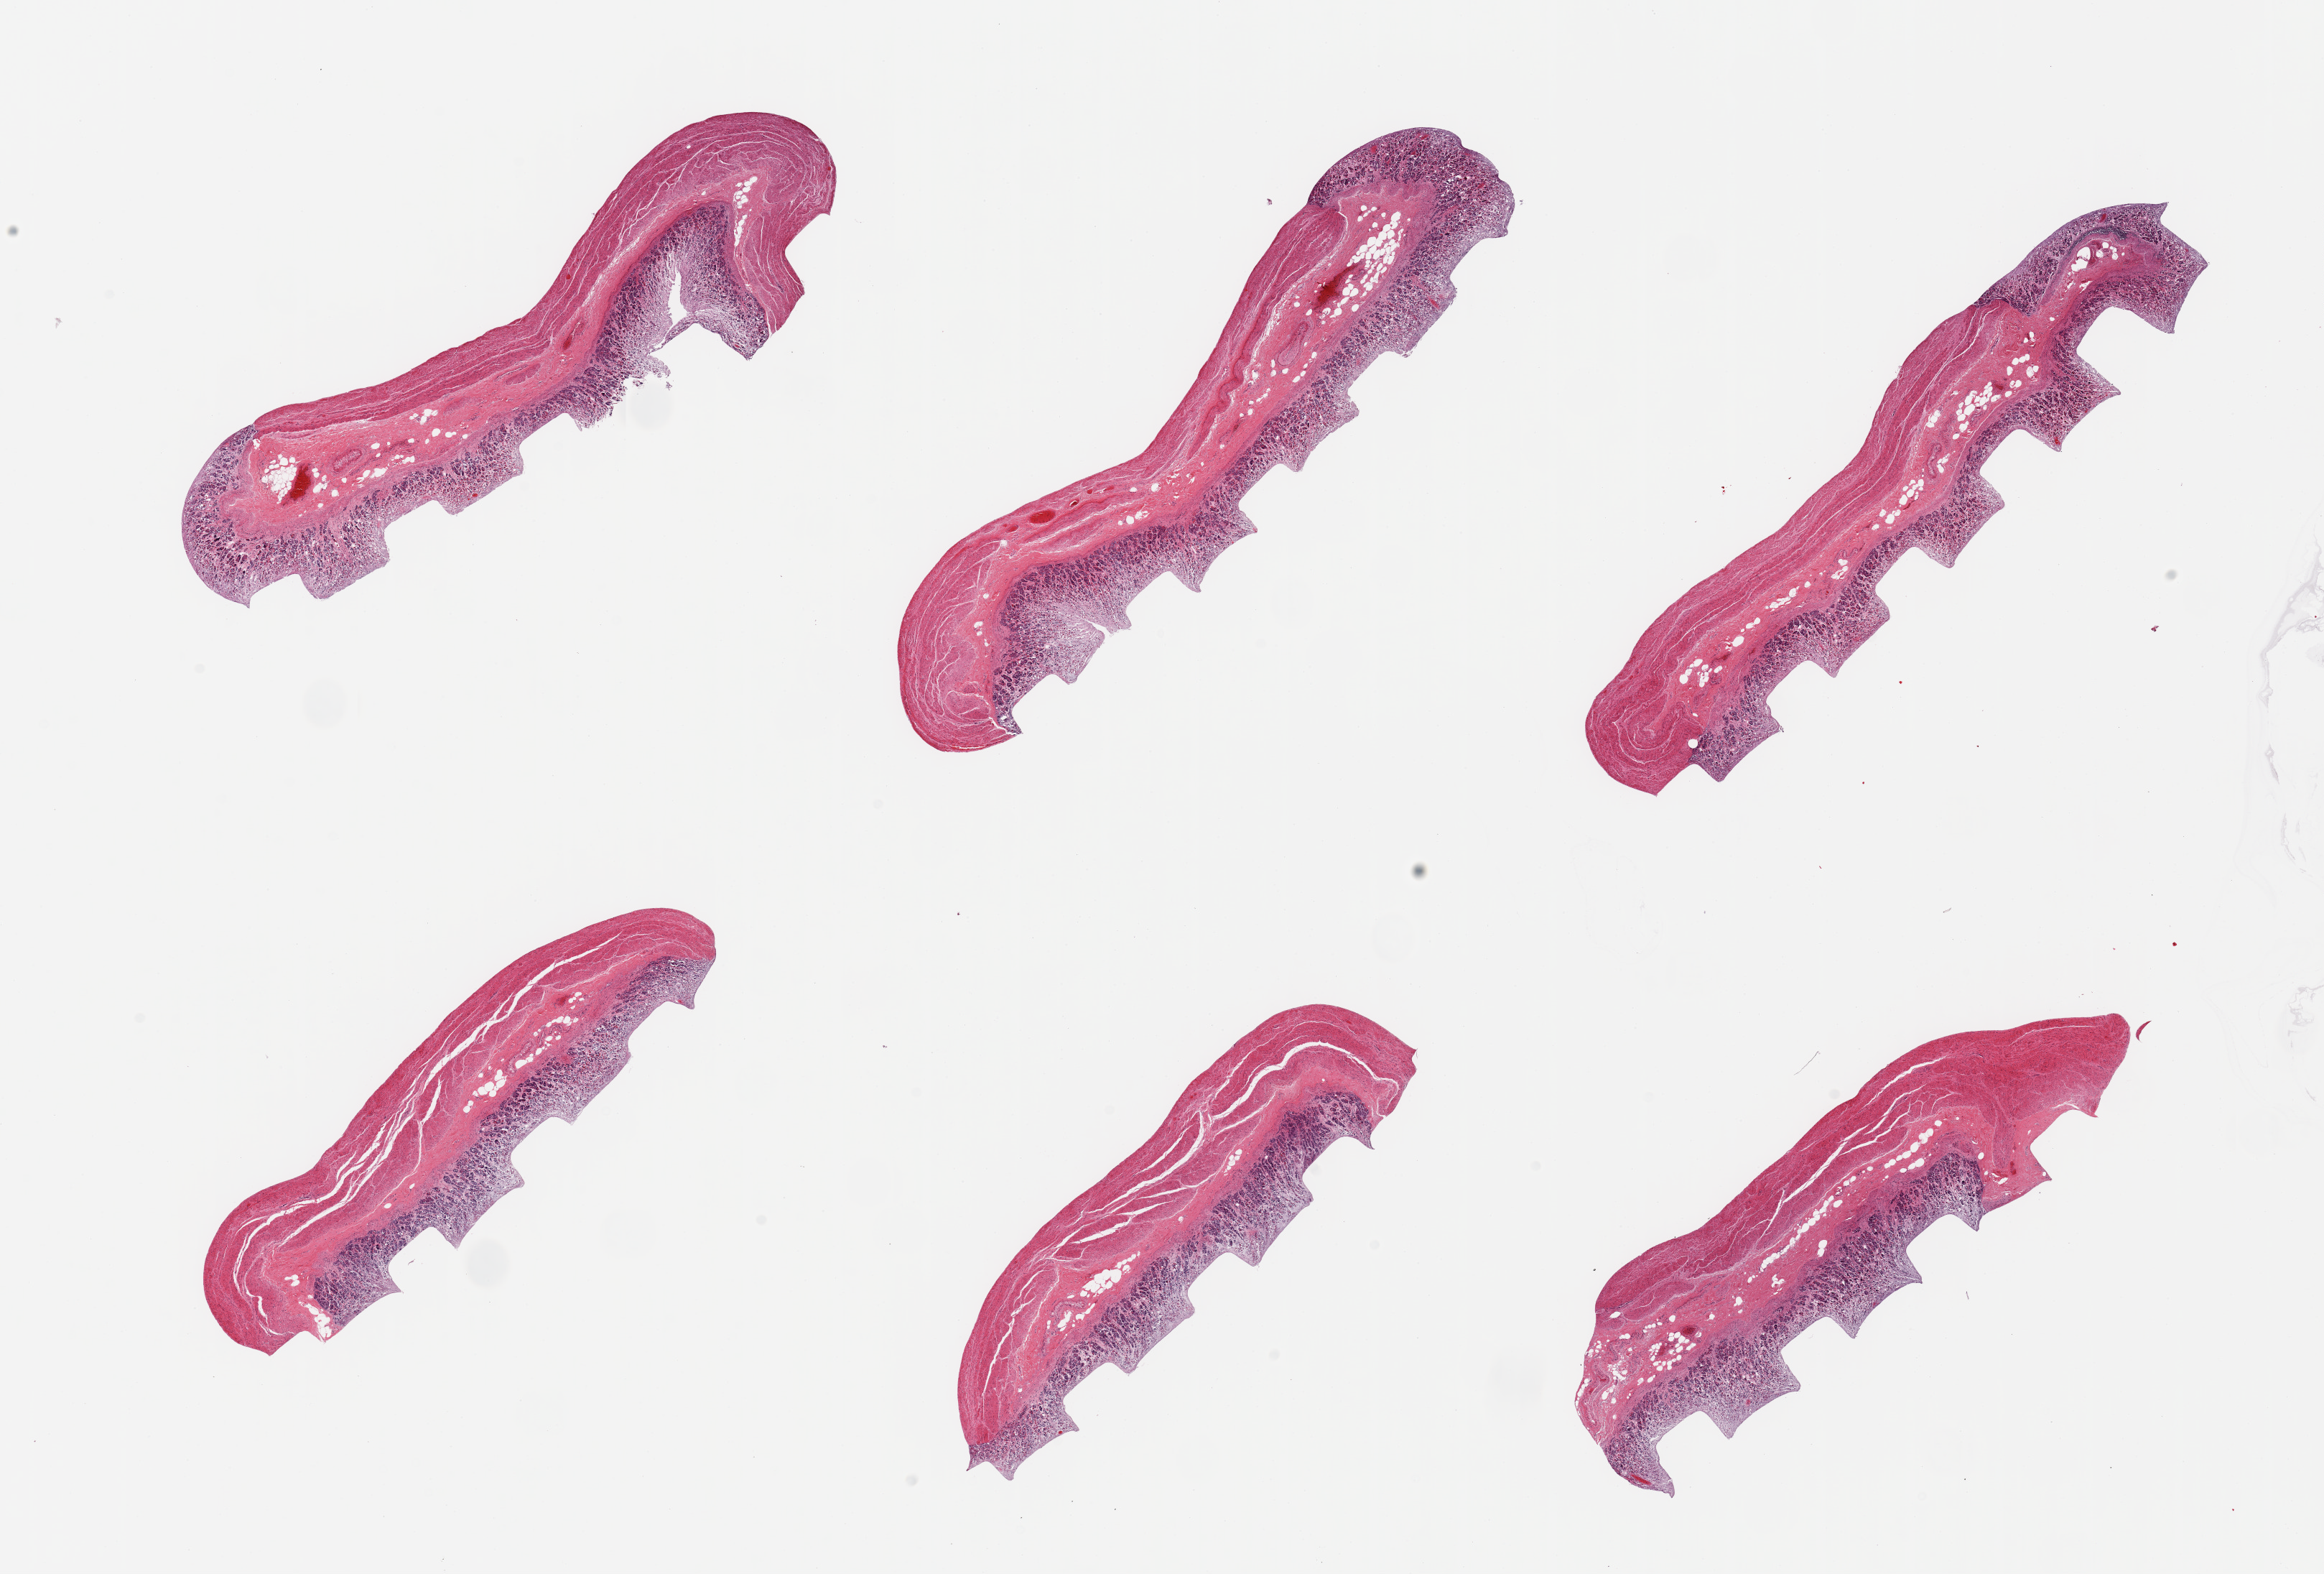
H&E whole-slide image, brightfield, whole scanned area (about 25.6 x 17.3 mm, acquisition: 20x scan) shown as a low-resolution overview. PAXgene-fixed paraffin-embedded (PFPE) section. Sampled site (target tissue): stomach. Tissue donor sample. Male donor.
Reviewer comment on this tissue sample: 6 pieces; superficial mucosal glands autolyzed, deep glands in better shape.